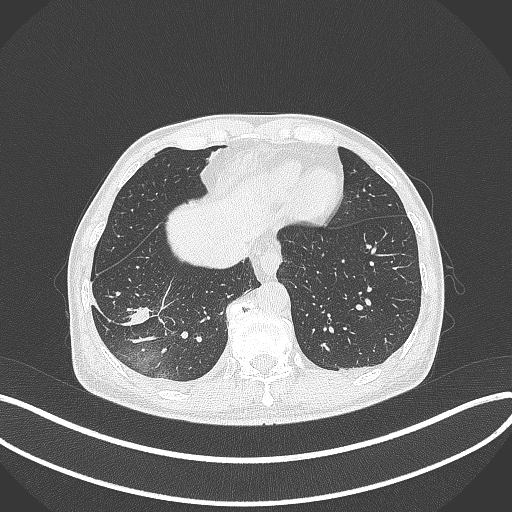
Chest CT, one axial slice. Position 89 of 388 along the scan axis. 120 kVp. Lung window (W 1500 / L -600 HU). 512 × 512 image matrix, field of view 400 × 400 mm. Patient: male, 64 years. From the clinical record (not read from this slice): clinical TNM (as recorded): T3 N0 M0.
Annotated regions visible in this slice (rectangle marked by the reading radiologist):
- lung tumour (recorded histology: adenocarcinoma): bounding box (x1, y1, x2, y2) in pixels: (125, 303, 158, 328)